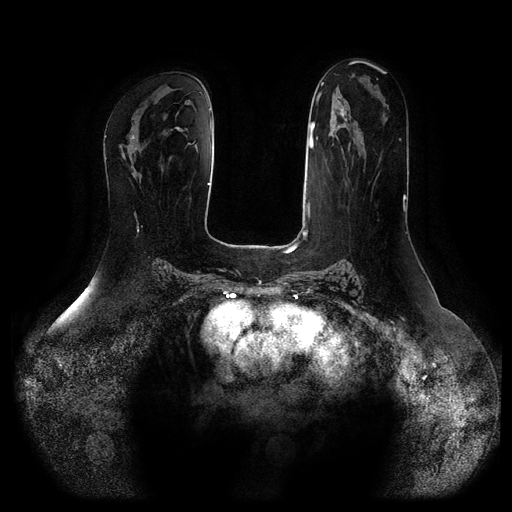
Breast MRI (dynamic contrast-enhanced, multi-phase), one axial slice. Position 48 of 116 along the scan axis. Dynamic contrast-enhanced series, time point 2 of 5 at this slice position (early post-contrast). 1.5 T. TE 2.5 ms, TR 5.2 ms. 2 mm slice thickness. 512 × 512 image matrix, field of view 400 × 400 mm. Female patient, age 66 years.
Outlined on this slice (semi-automatic segmentation, software-assisted and operator-edited):
- breast lesion (labelled 'tumour' in the annotation; benign lesions carry a separate 'benign' label): bounding box (x1, y1, x2, y2) in pixels: (171, 126, 181, 132)